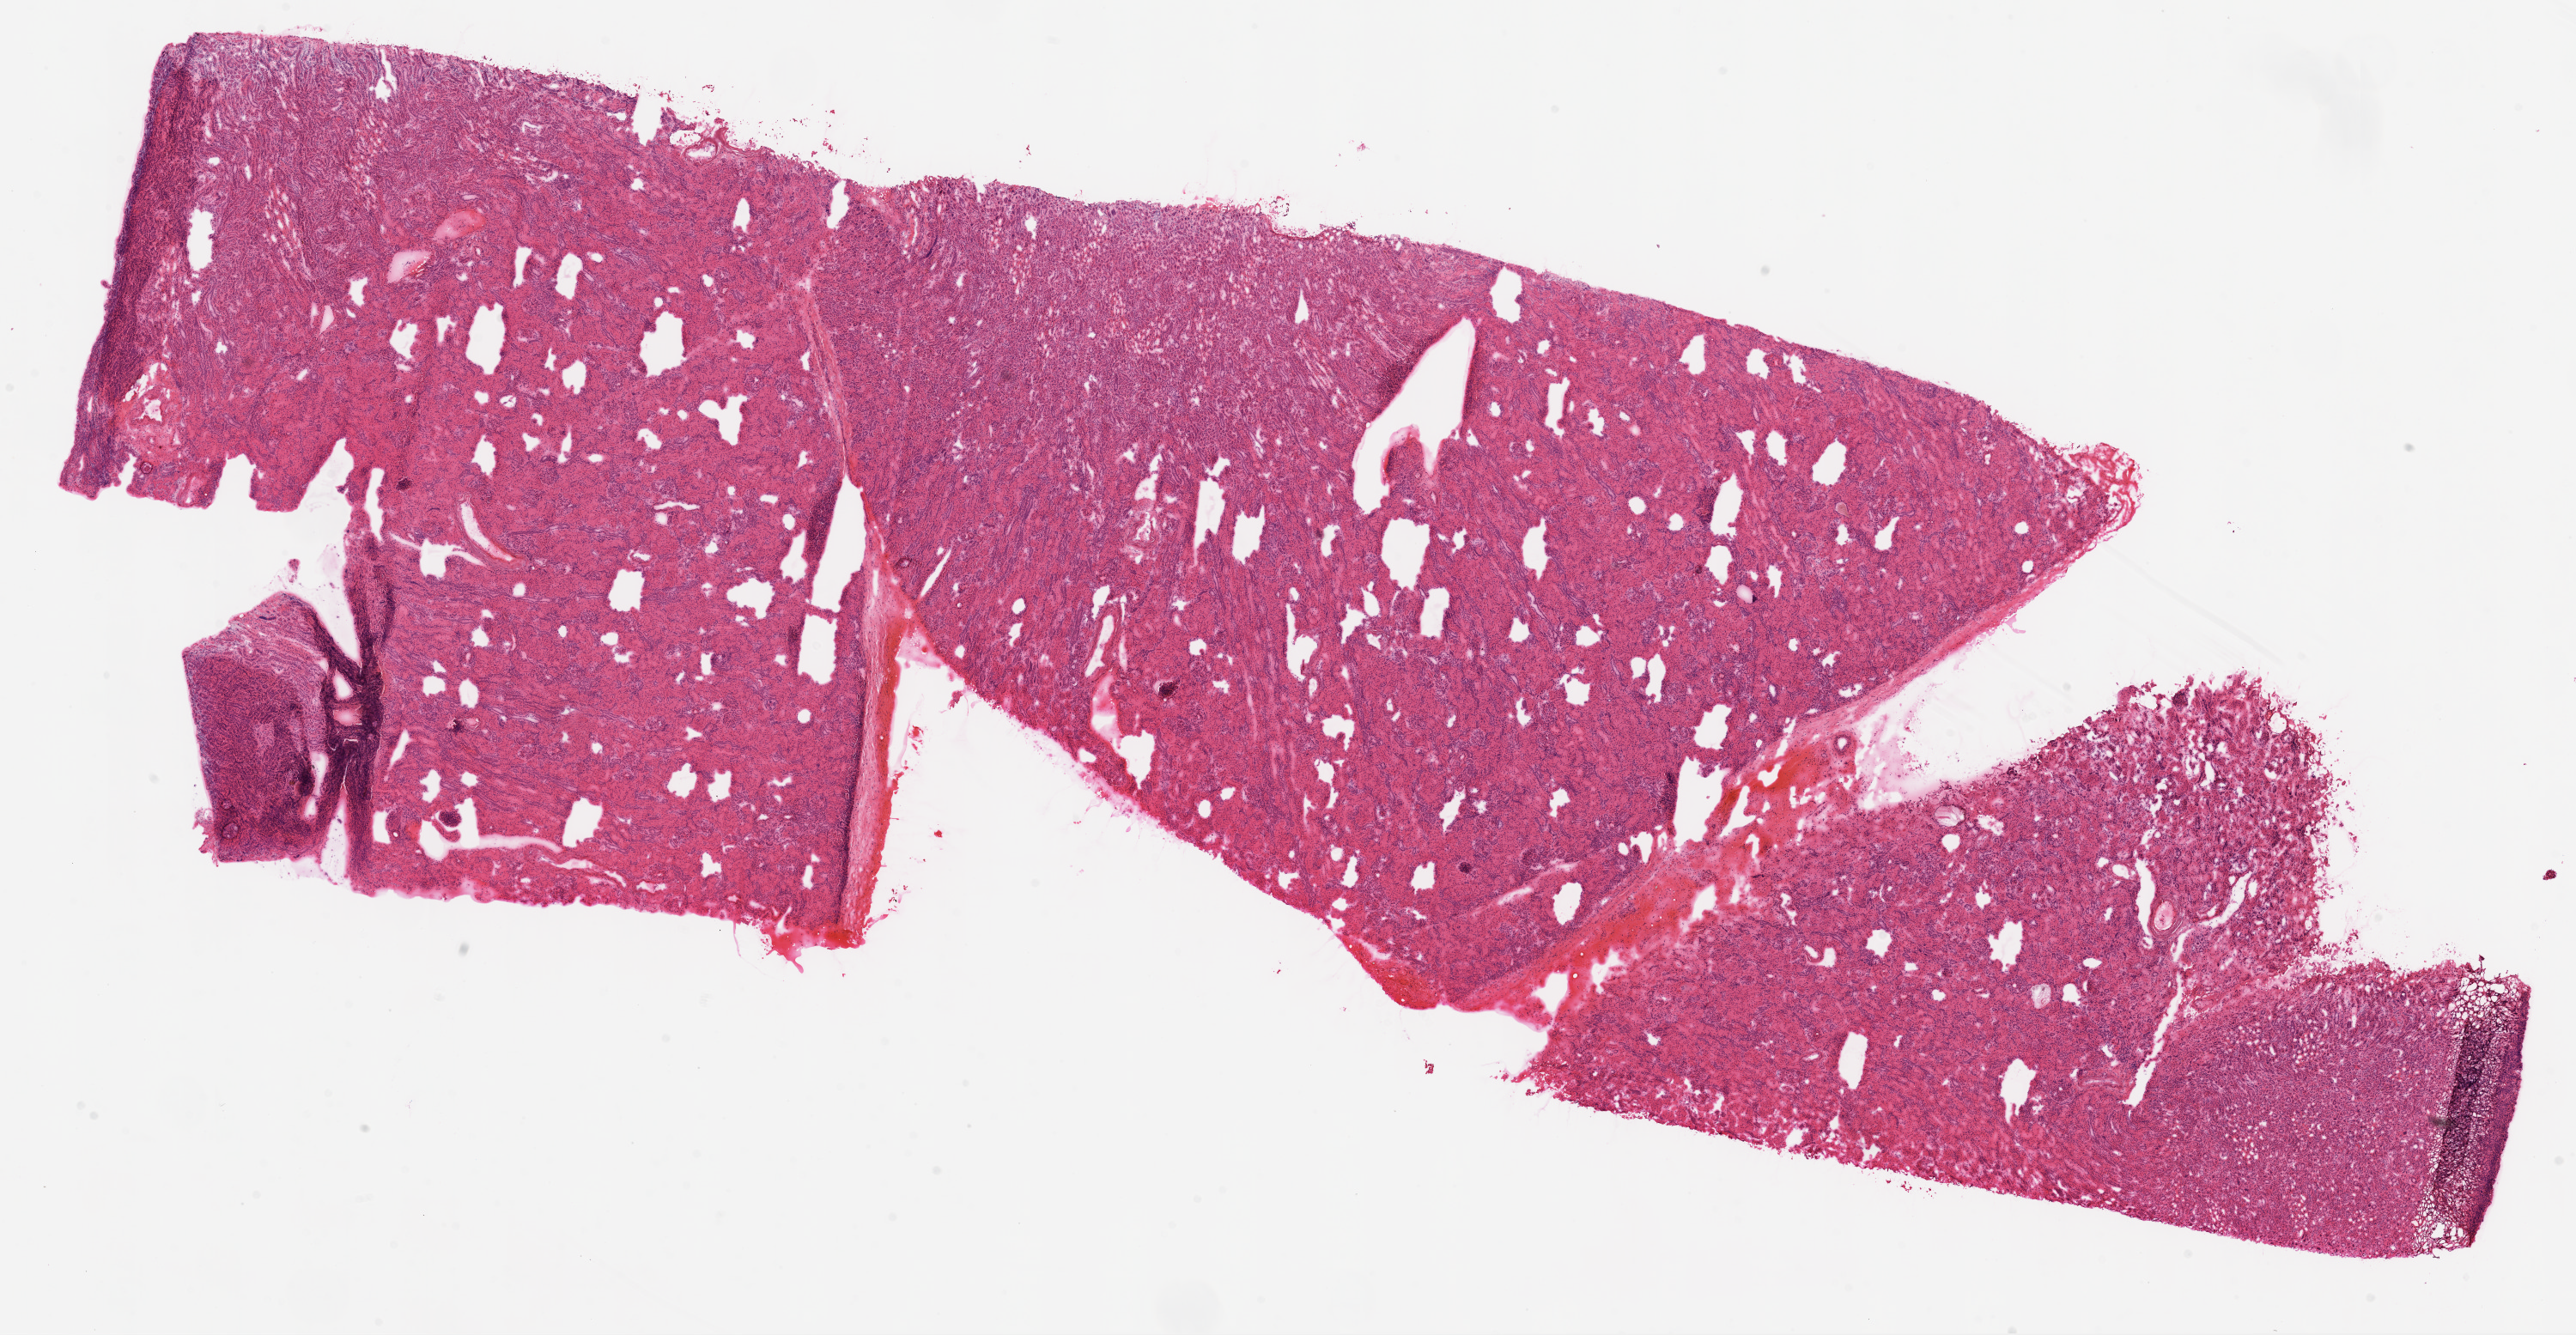
Digitized Hematoxylin and eosin (H&E) stained tissue section (whole slide), a low-resolution overview of the entire scanned area, about 24.1 x 12.5 mm; frozen section from the top of the tissue portion; sample: solid tissue normal (non-tumour tissue), kidney. Female, age 79 years at initial diagnosis.
This section: solid tissue normal (non-tumour) sample from the same patient. Patient diagnosis: Clear cell adenocarcinoma, NOS.